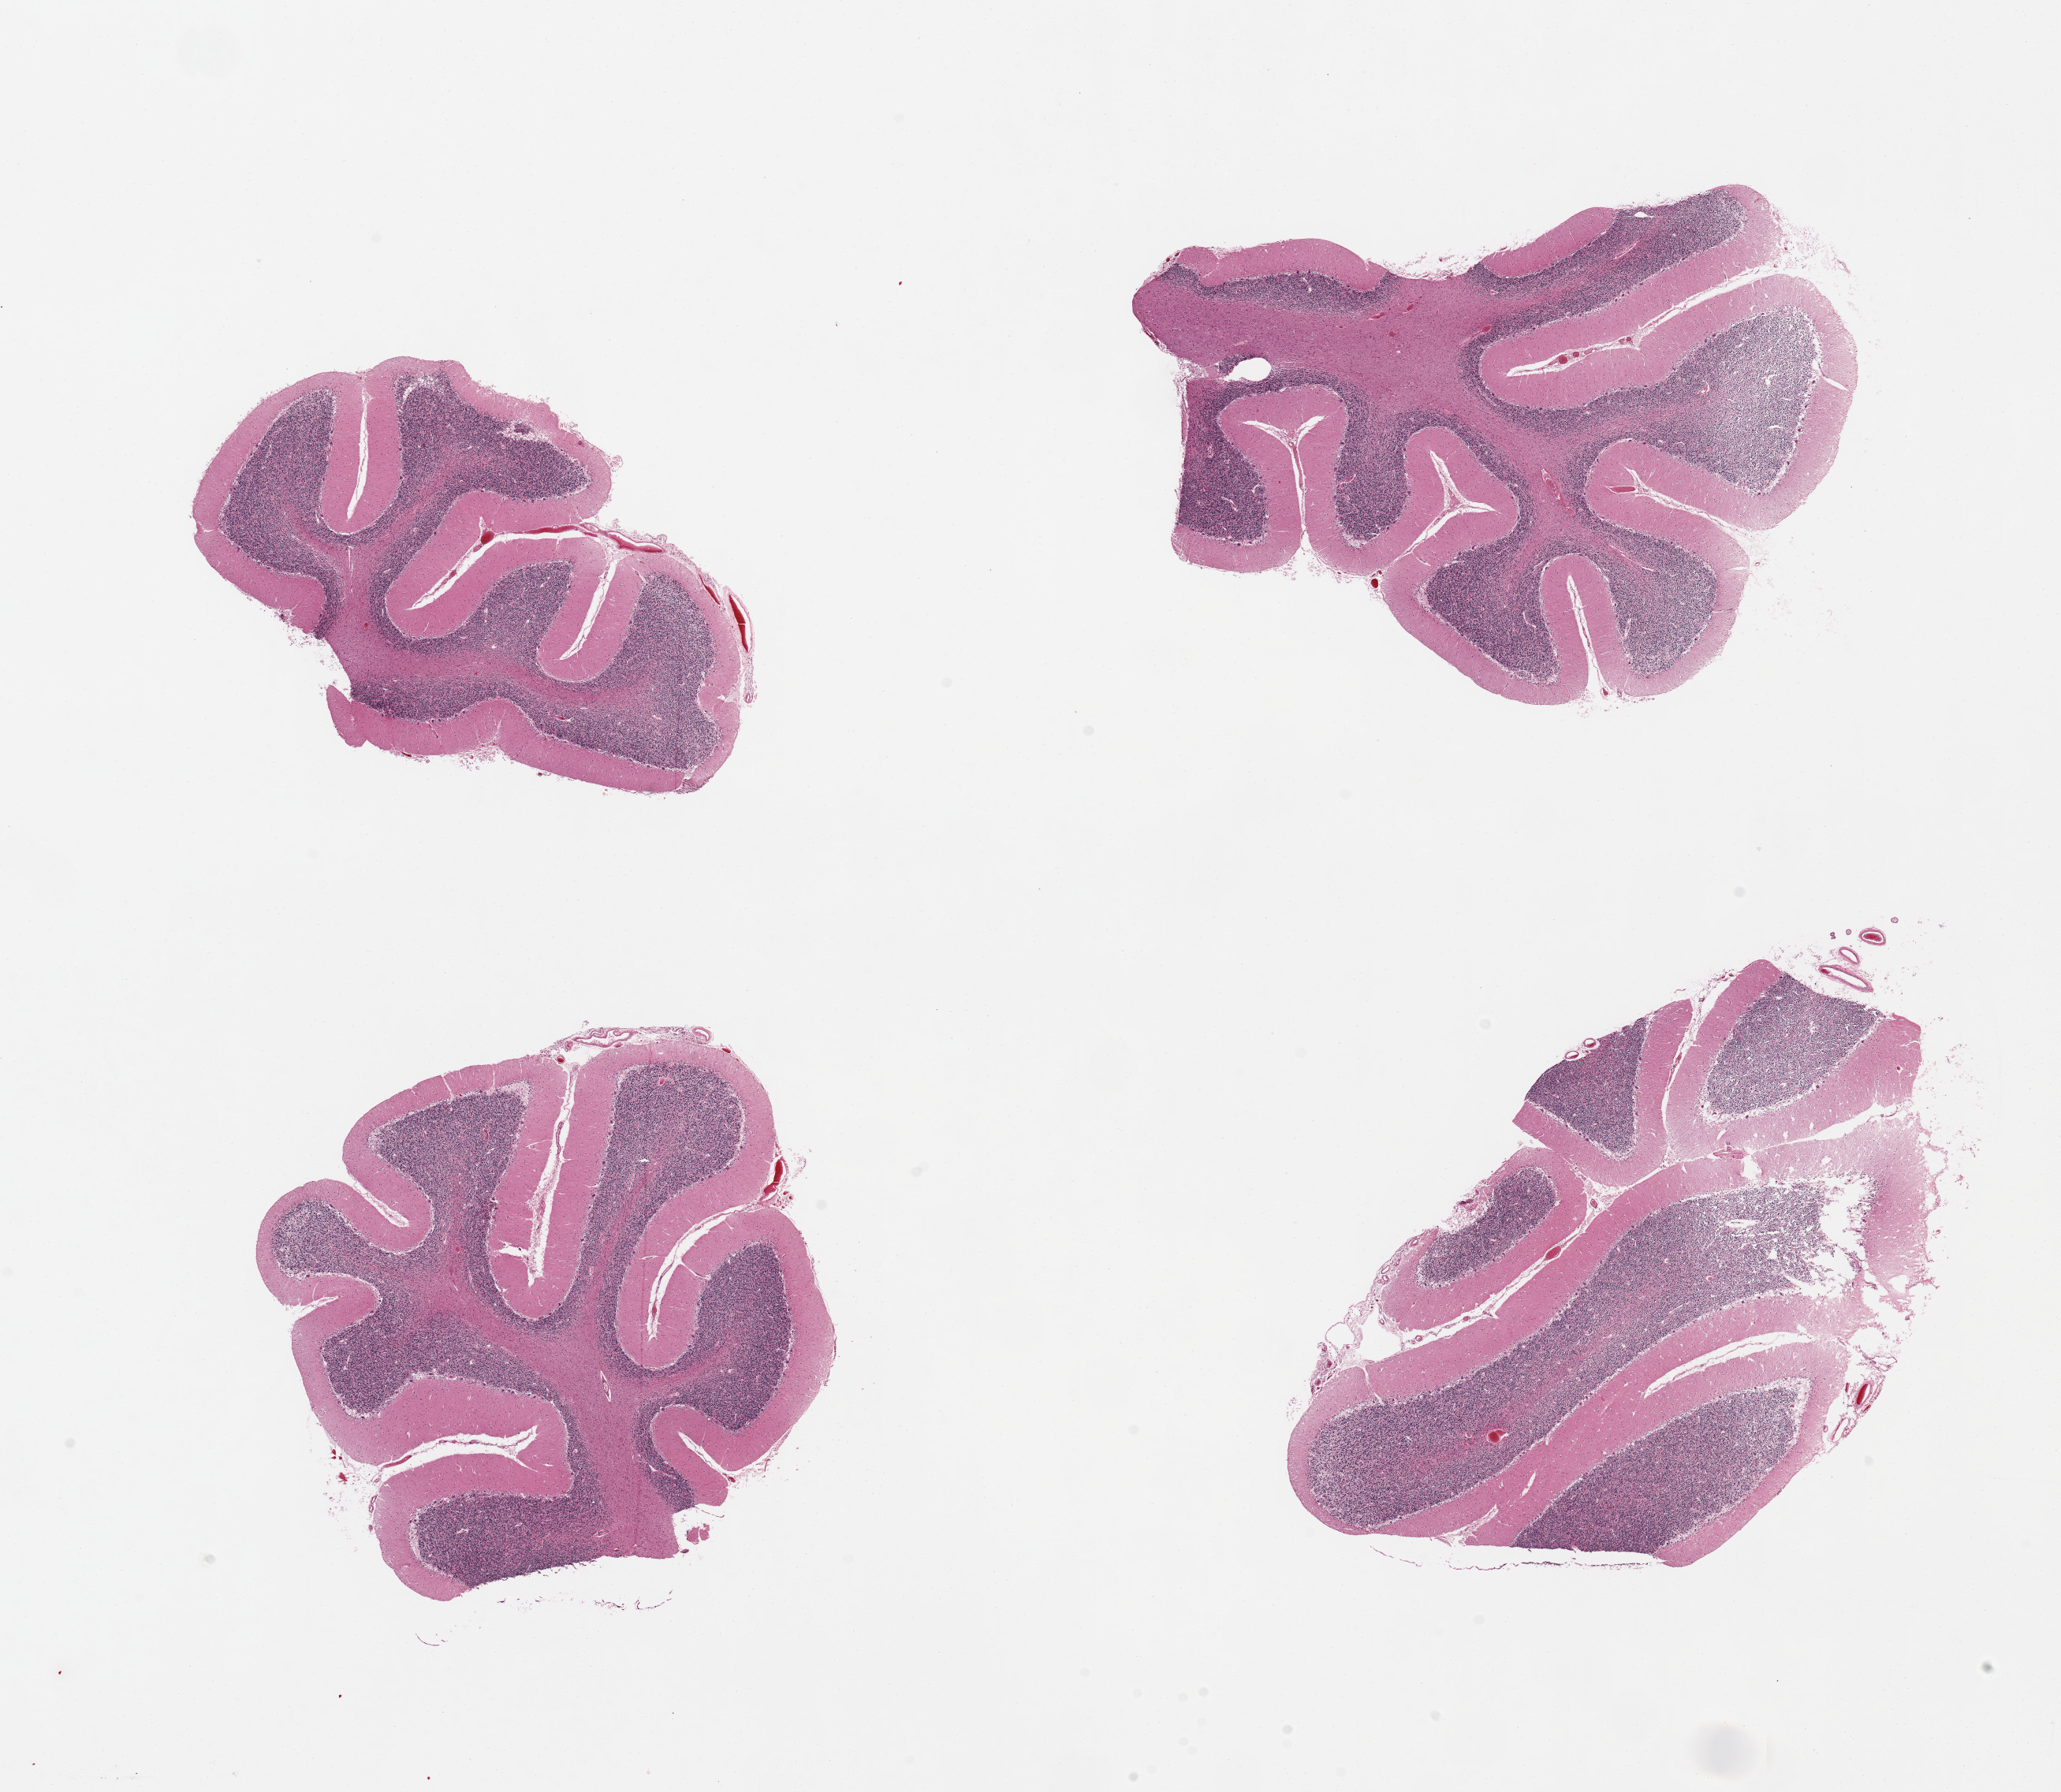
H&E whole-slide image — low-resolution overview of the scanned area, about 20.7 x 18.0 mm (slide scanned at 20x); PAXgene-fixed paraffin-embedded (PFPE) section; section of cerebellum (target tissue); donor tissue sample. Donor: male.
Review note (as recorded): 4 pieces; Purkinje cells well-visualized with some autolytic neuronal condensation.